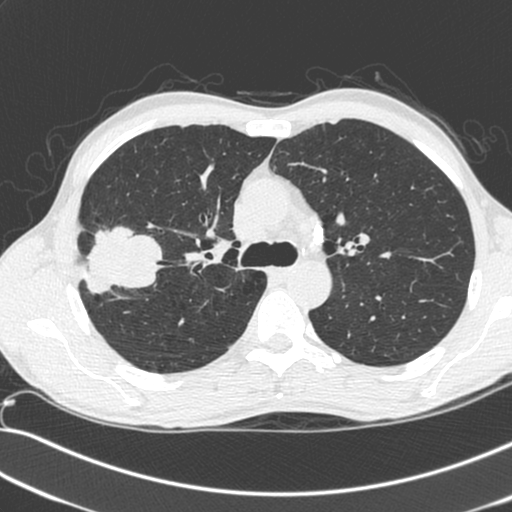
Chest CT (low-dose screening protocol), one axial image; first (baseline) screen; lung window (W 1500 / L -600 HU); 512 × 512 image matrix. Male, age 55 years at enrolment. Current smoker at enrolment.
Lesion marked by an expert reader, box from (x=70, y=229) to (x=153, y=303) px. Screening reader's record for this exam (one nodule recorded; not confirmed to be the boxed lesion): non-calcified nodule or mass ≥4 mm, right upper lobe, 52 × 39 mm, spiculated (stellate) margins, soft tissue attenuation. Lung cancer was diagnosed 25 days after this screen: large cell neuroendocrine carcinoma, right upper lobe, poorly differentiated (G3), stage IIB (AJCC 6th edition), 49 mm at pathology.